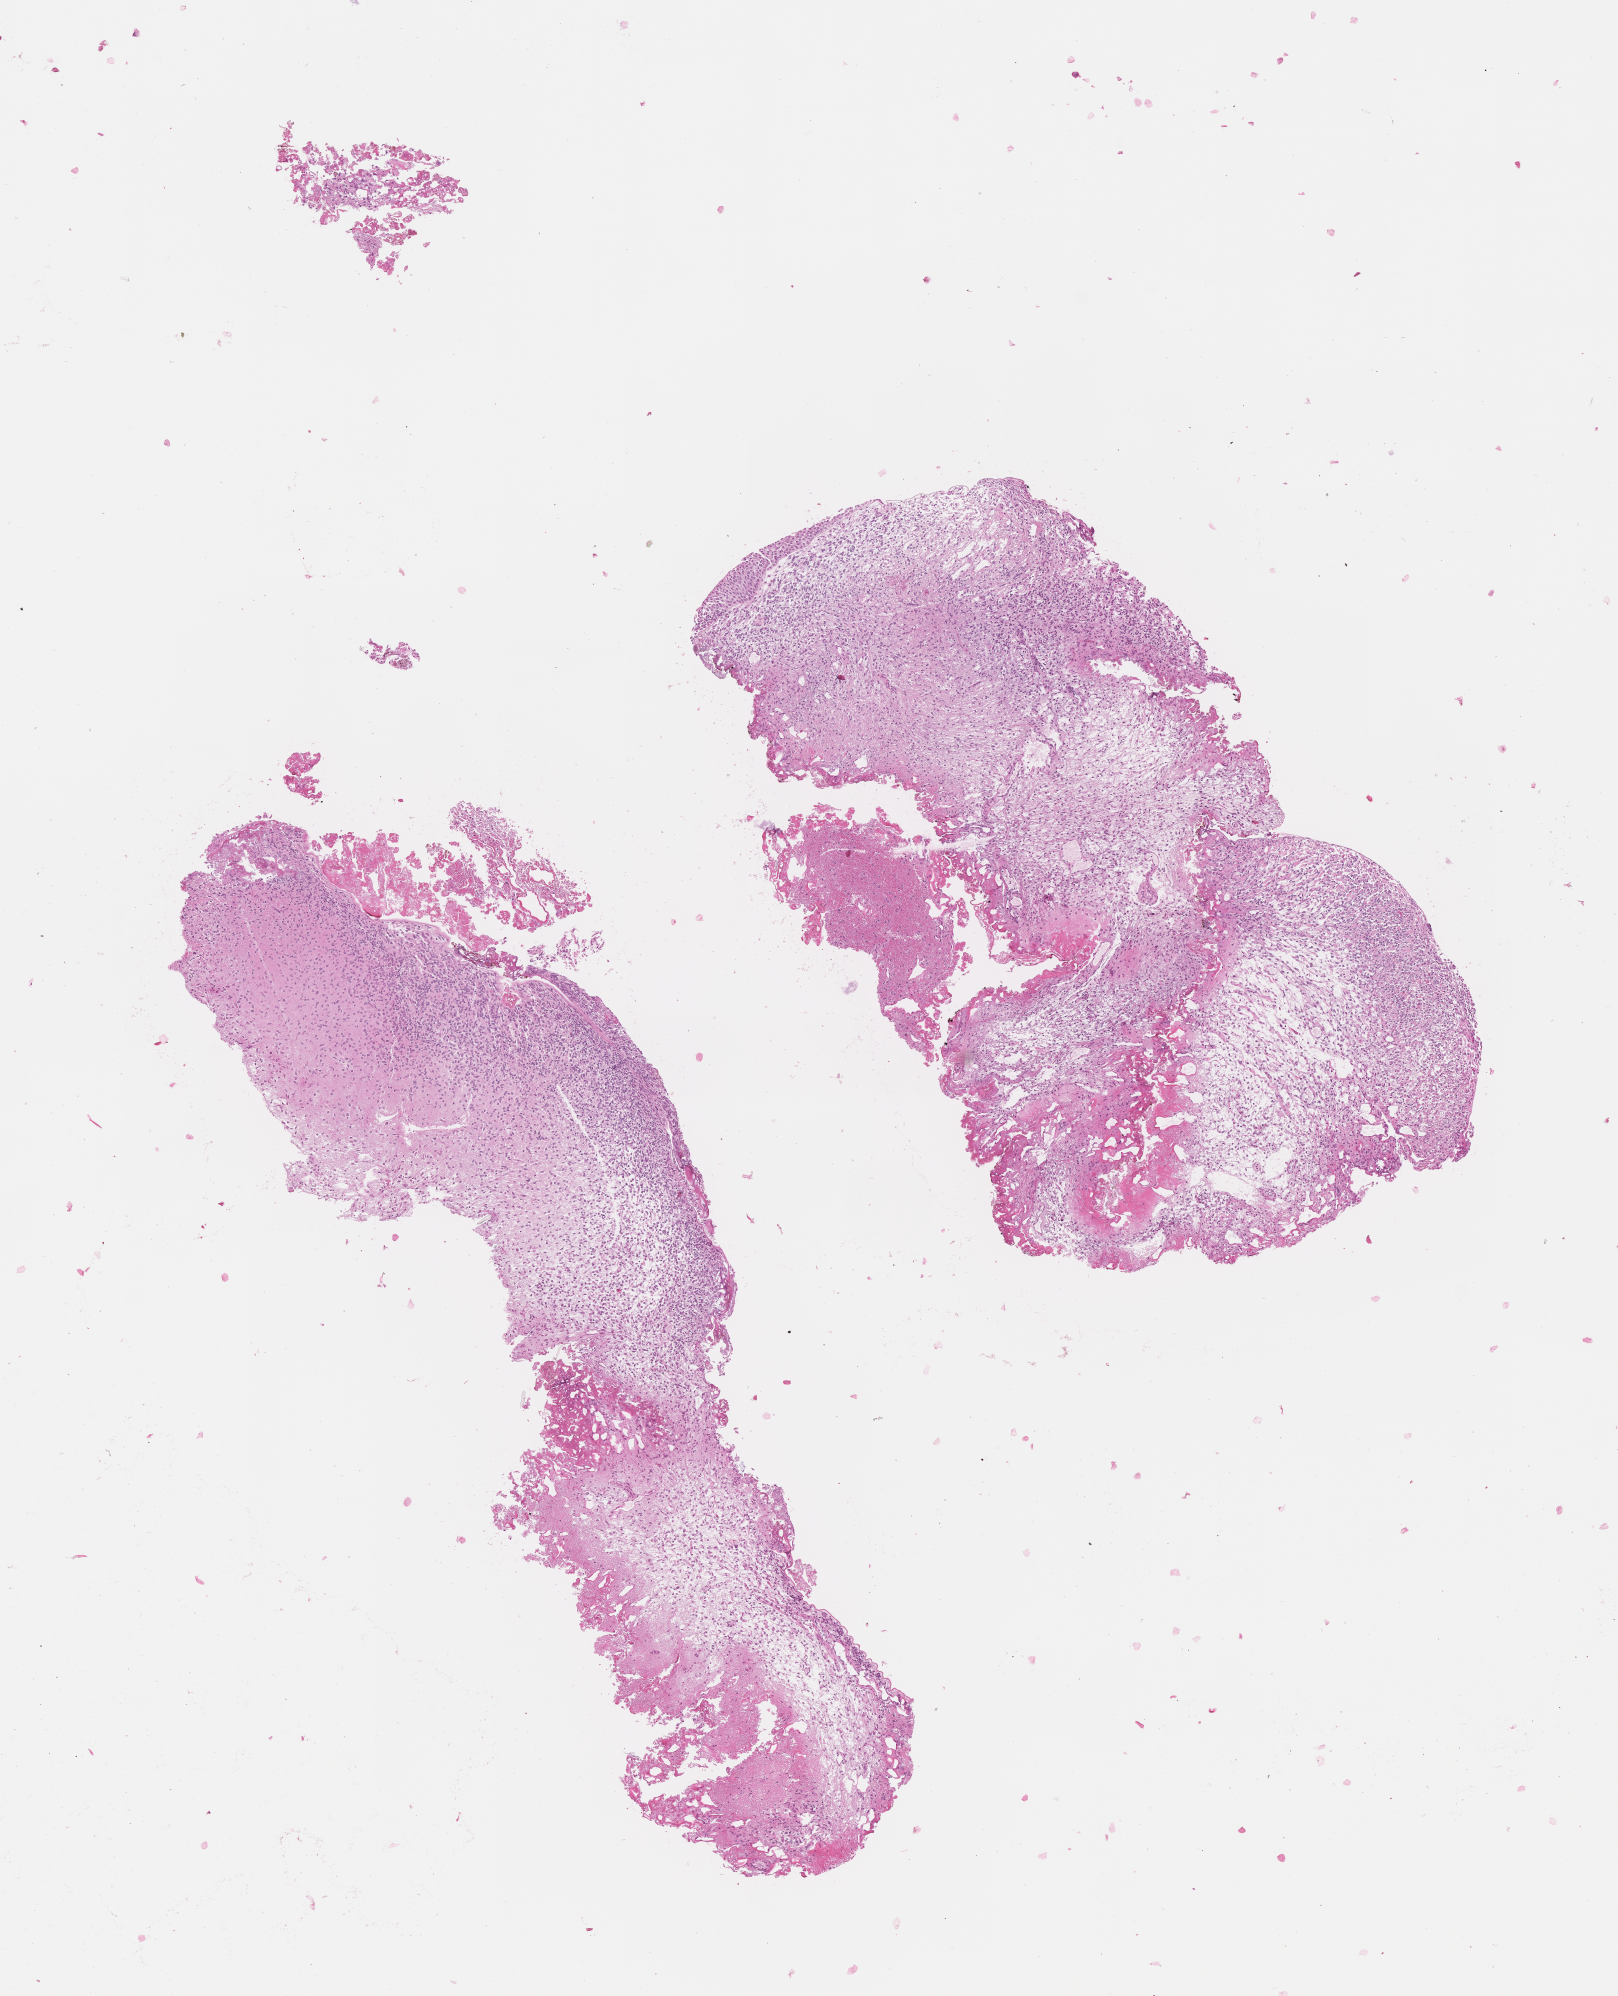
Digitized H&E-stained section of tumor tissue, a low-resolution overview of the entire scanned area, about 6.5 x 8.1 mm. Formalin-fixed, paraffin-embedded (FFPE) tissue. Site: bladder. Male patient, age at diagnosis 1.8 years.
Metastatic status at presentation (as recorded): non-metastatic (confirmed). Stage (as recorded): 3. Diagnosis: rhabdomyosarcoma; histological classification: botryoid.